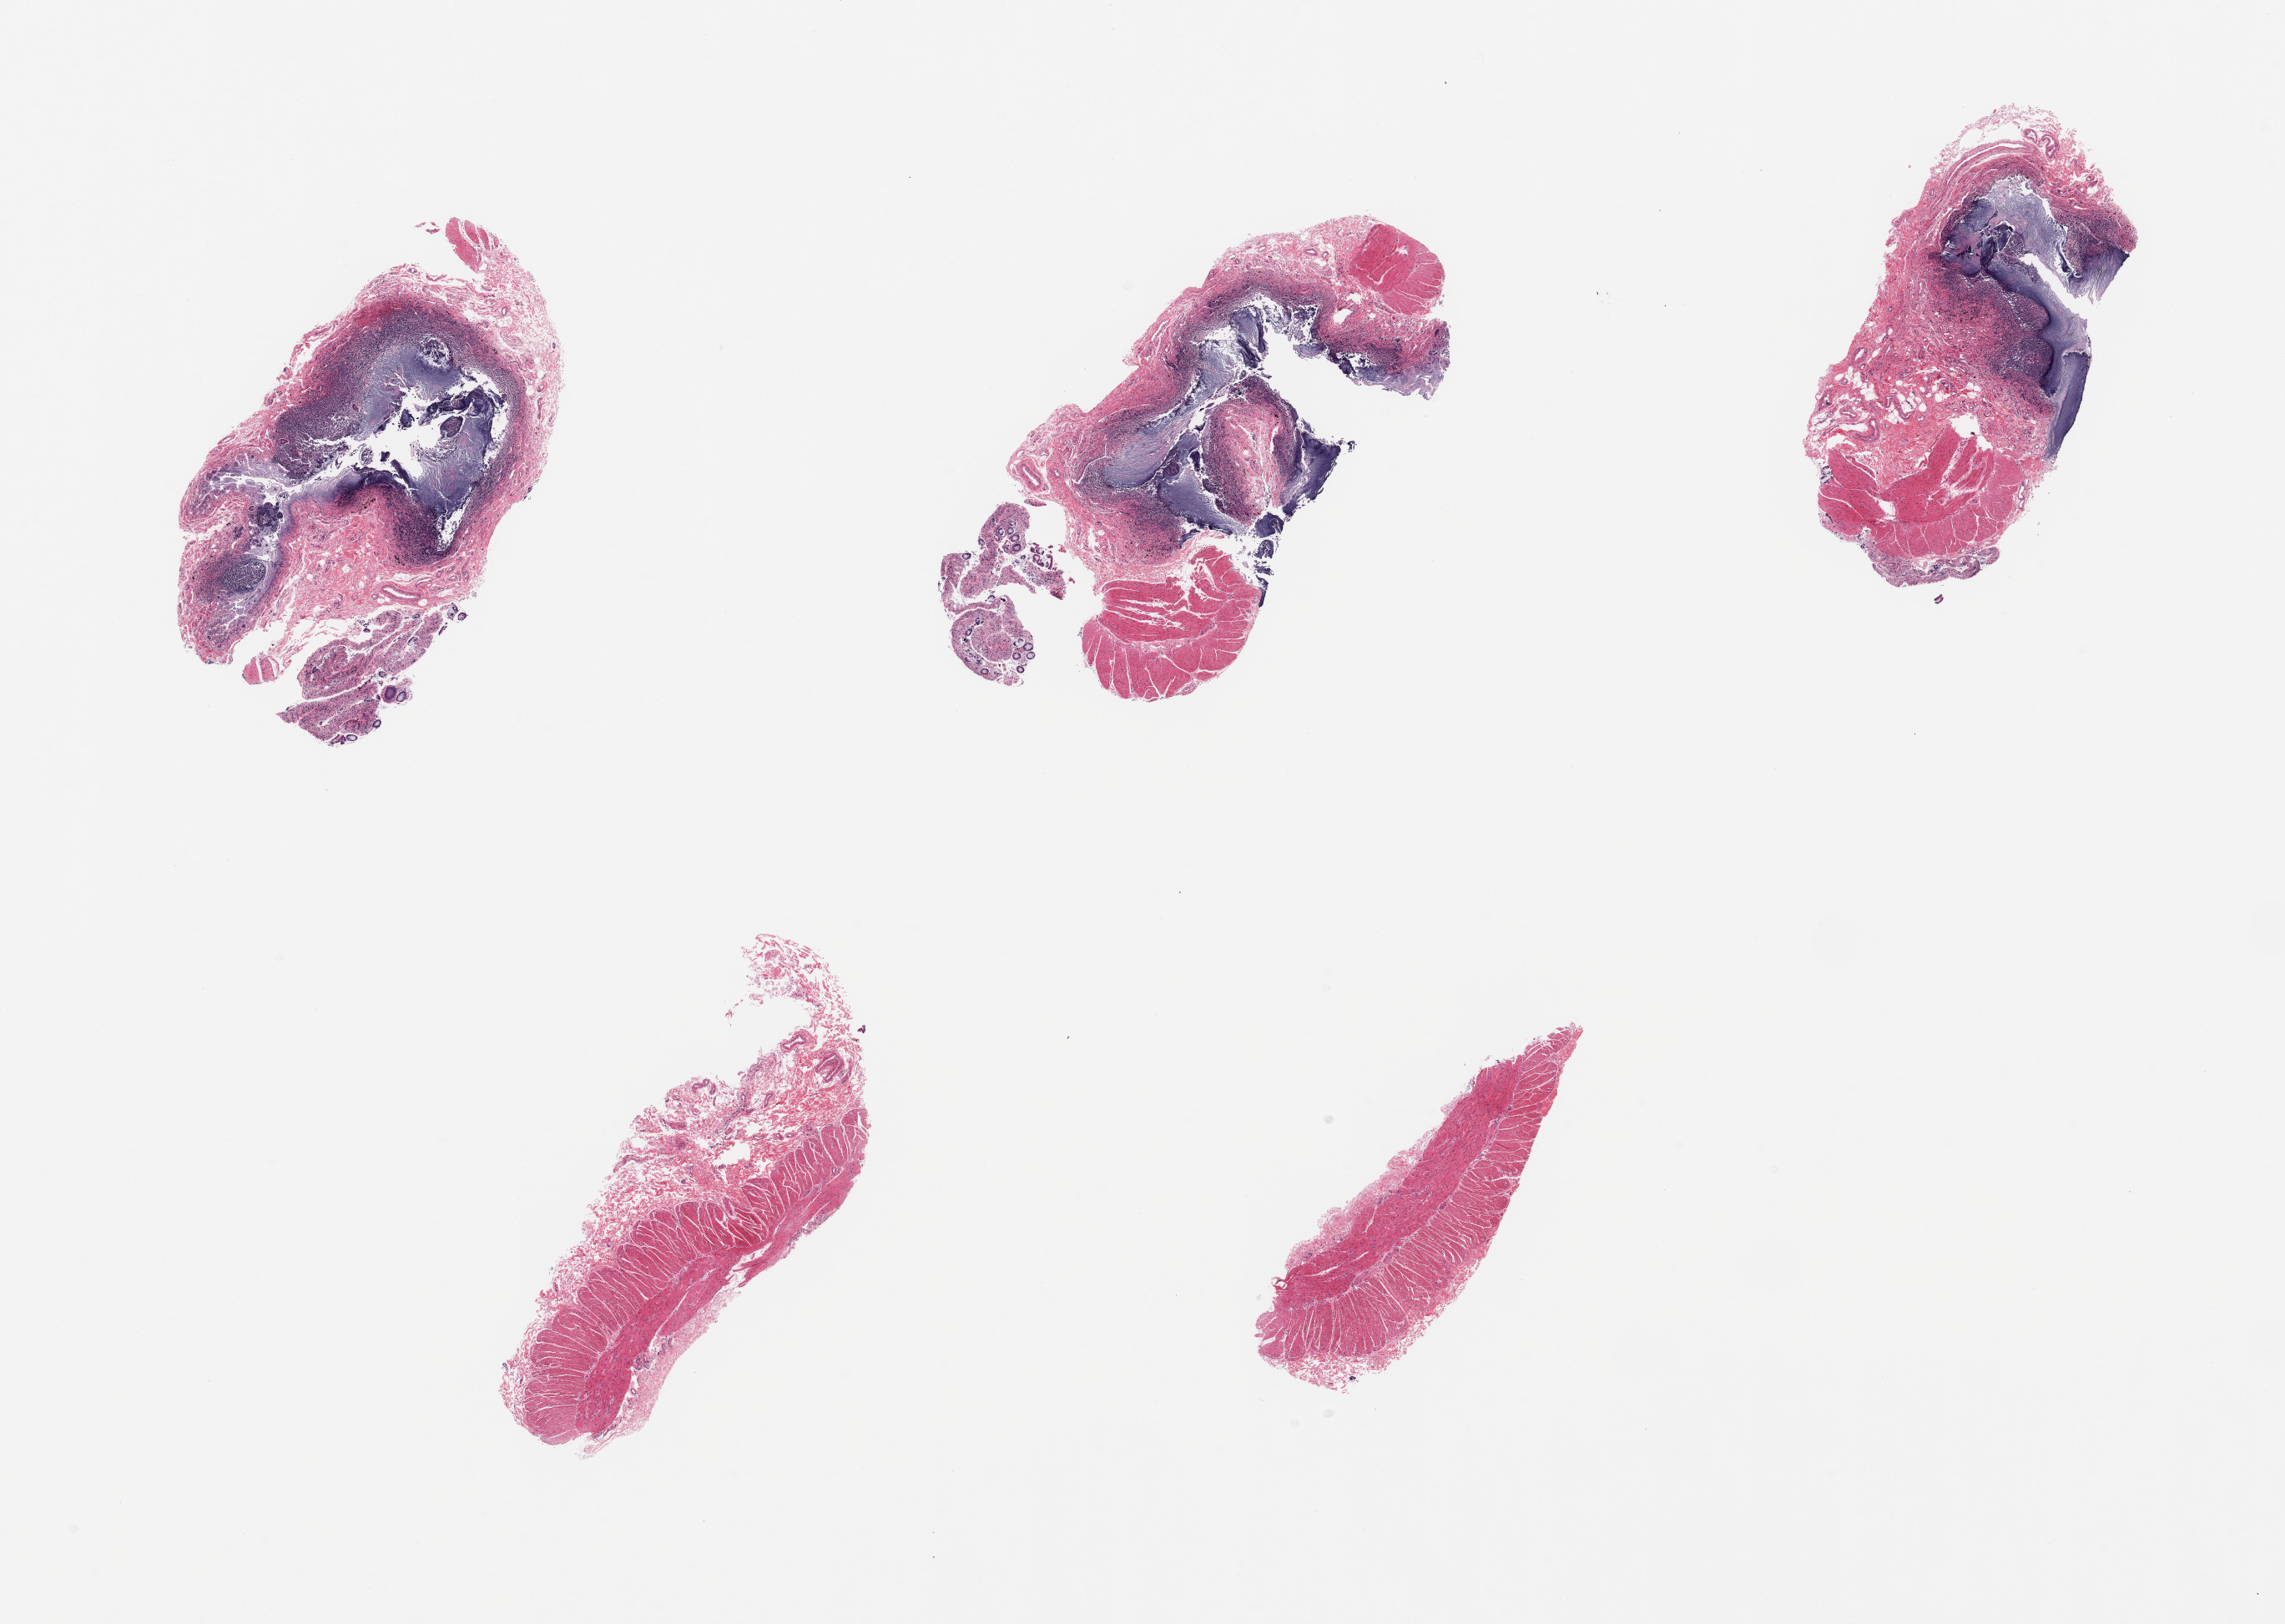
Digitized hematoxylin and eosin (H&E)-stained section — shown as a low-resolution overview of the whole scanned area (about 21.7 x 15.4 mm, slide scanned at 20x); PAXgene-fixed, paraffin-embedded tissue; section of ileum (target tissue); donor tissue sample. Donor: female.
* pathologist's review note for this sample: 5 pieces; excessive autolysis of lymphoid tissue; muscularis propria in 4 of 5 pieces